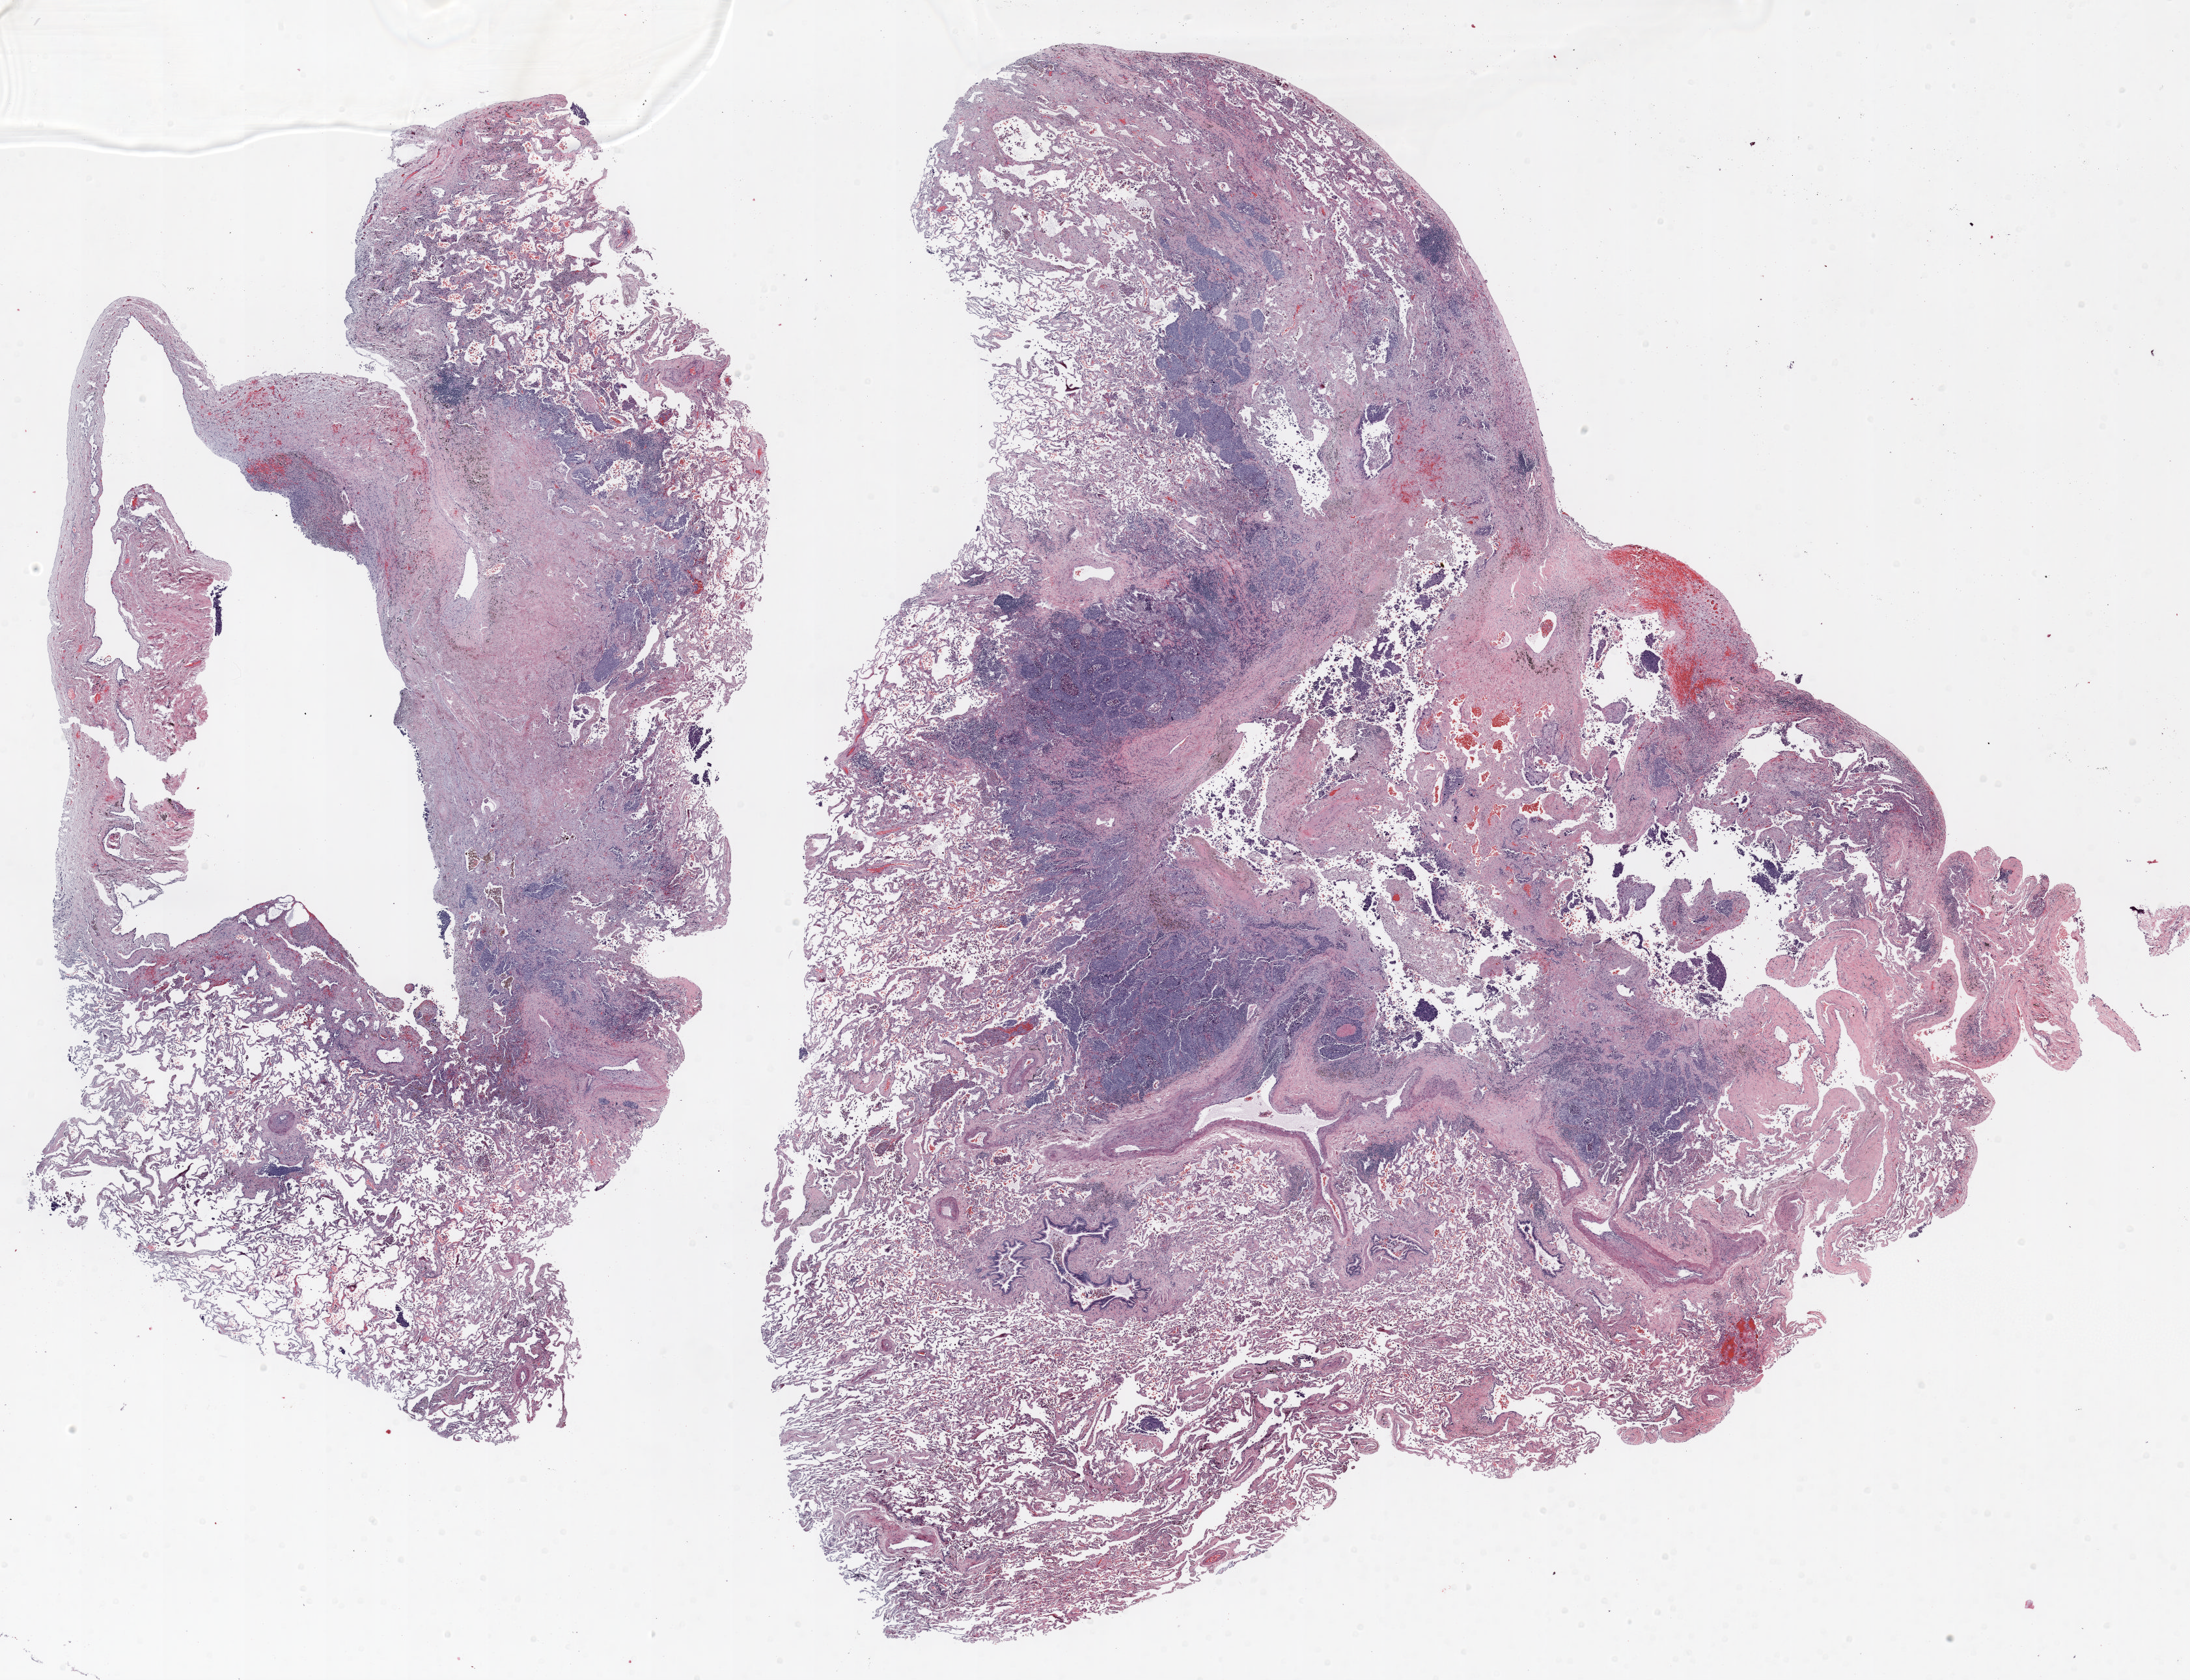
H&E-stained whole-slide image, a low-resolution overview of the entire scanned area, about 27.0 x 20.7 mm; FFPE section; lung. Male, age 64 at enrolment. Current smoker at enrolment.
Participant's lung-cancer diagnosis: Adenocarcinoma, NOS.